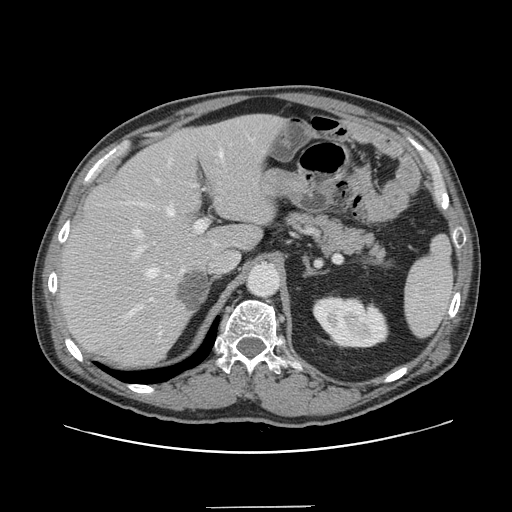
Contrast-enhanced abdominal CT, one axial slice; position 98 of 139 along the scan axis; 120 kVp; intravenous contrast given; soft-tissue window (W 400 / L 40 HU); 512 × 512 image matrix, field of view 397 × 397 mm. Male patient, age 64 years. Case-level facts recorded for this patient, not image findings: diagnosis: colorectal cancer liver metastases, imaged before liver resection; multiple liver metastases: yes; largest metastasis: 3.5 cm.
Structures marked on this image (manually delineated by an expert):
- hepatic veins: box from (x=128, y=139) to (x=253, y=334) px
- liver: (x=61, y=116)–(x=282, y=365)
- planned liver remnant (the part of the liver to remain after resection): (x=61, y=116)–(x=272, y=365)
- portal vein (with intrahepatic branches): (x=132, y=185)–(x=207, y=273)
- liver metastasis: (x=178, y=271)–(x=207, y=312)